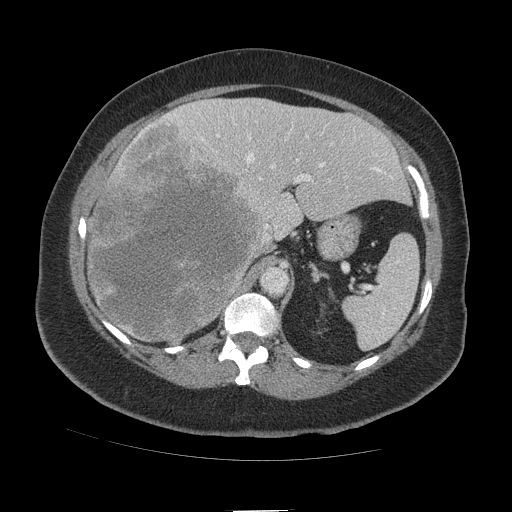
Contrast-enhanced abdominal CT (liver protocol), one axial slice; slice 68 of 109 in the series (ordered by position); reconstruction kernel STANDARD; 140 kVp; soft-tissue window (W 400 / L 40 HU); 2.5 mm slice thickness; 512 × 512 image matrix, field of view 420 × 420 mm. Case-level facts recorded for this patient, not image findings: diagnosis: hepatocellular carcinoma (patient treated with transarterial chemoembolisation; whether this scan precedes or follows treatment is not stated here); TNM stage (as recorded): Stage-IVB; Child-Pugh class: A; tumour differentiation: poorly differentiated; tumour nodularity: multinodular.
Structures marked on this image (semi-automatically segmented with operator editing):
- liver parenchyma outside the tumour (the mass and vessels are separate outlines, so this box may not span the whole liver): bounding box <88,98,410,342> (left, top, right, bottom; pixels)
- mass: <88,119,266,344>
- liver vessels: <138,113,382,227>